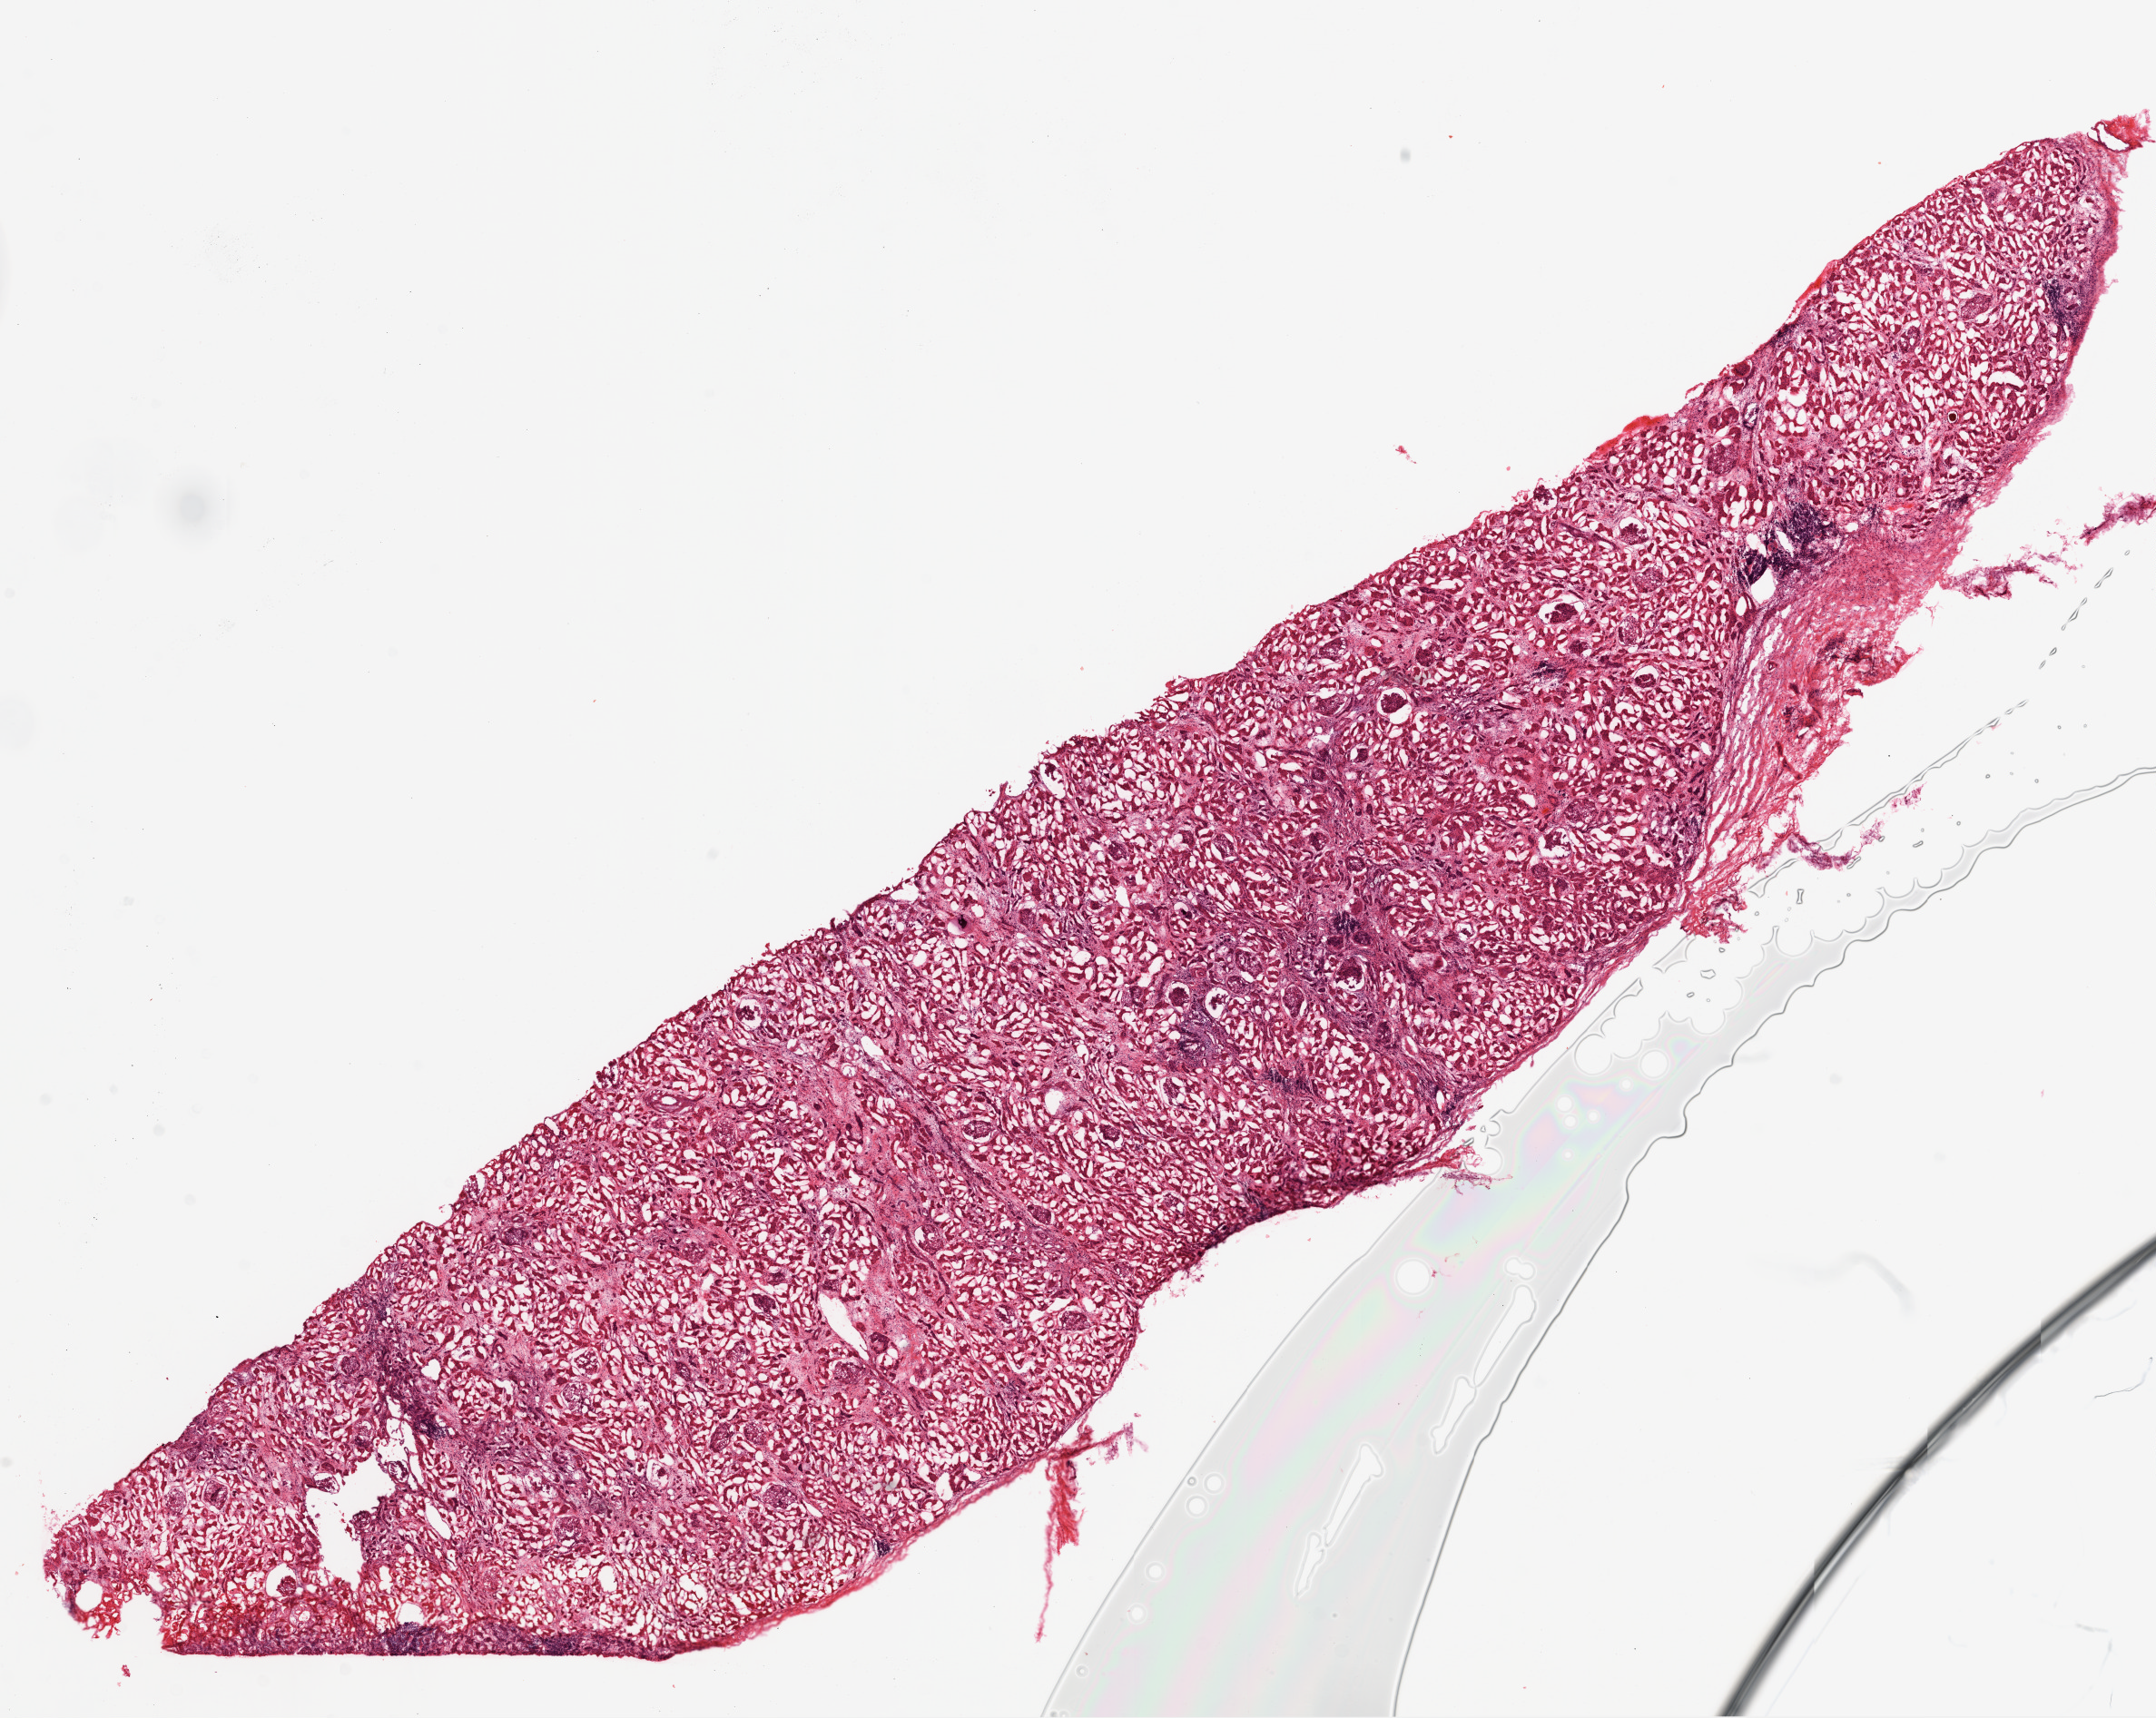
Digitized Hematoxylin and eosin (H&E) stained tissue section (whole slide), whole scanned area (about 19.1 x 15.2 mm, acquisition: 20x scan) shown as a low-resolution overview. Frozen section. Sample: solid tissue normal (non-tumour tissue), kidney. Male, age 68 years at initial diagnosis.
This section: solid tissue normal (non-tumour) sample from the same patient. Patient diagnosis: Clear cell adenocarcinoma, NOS.